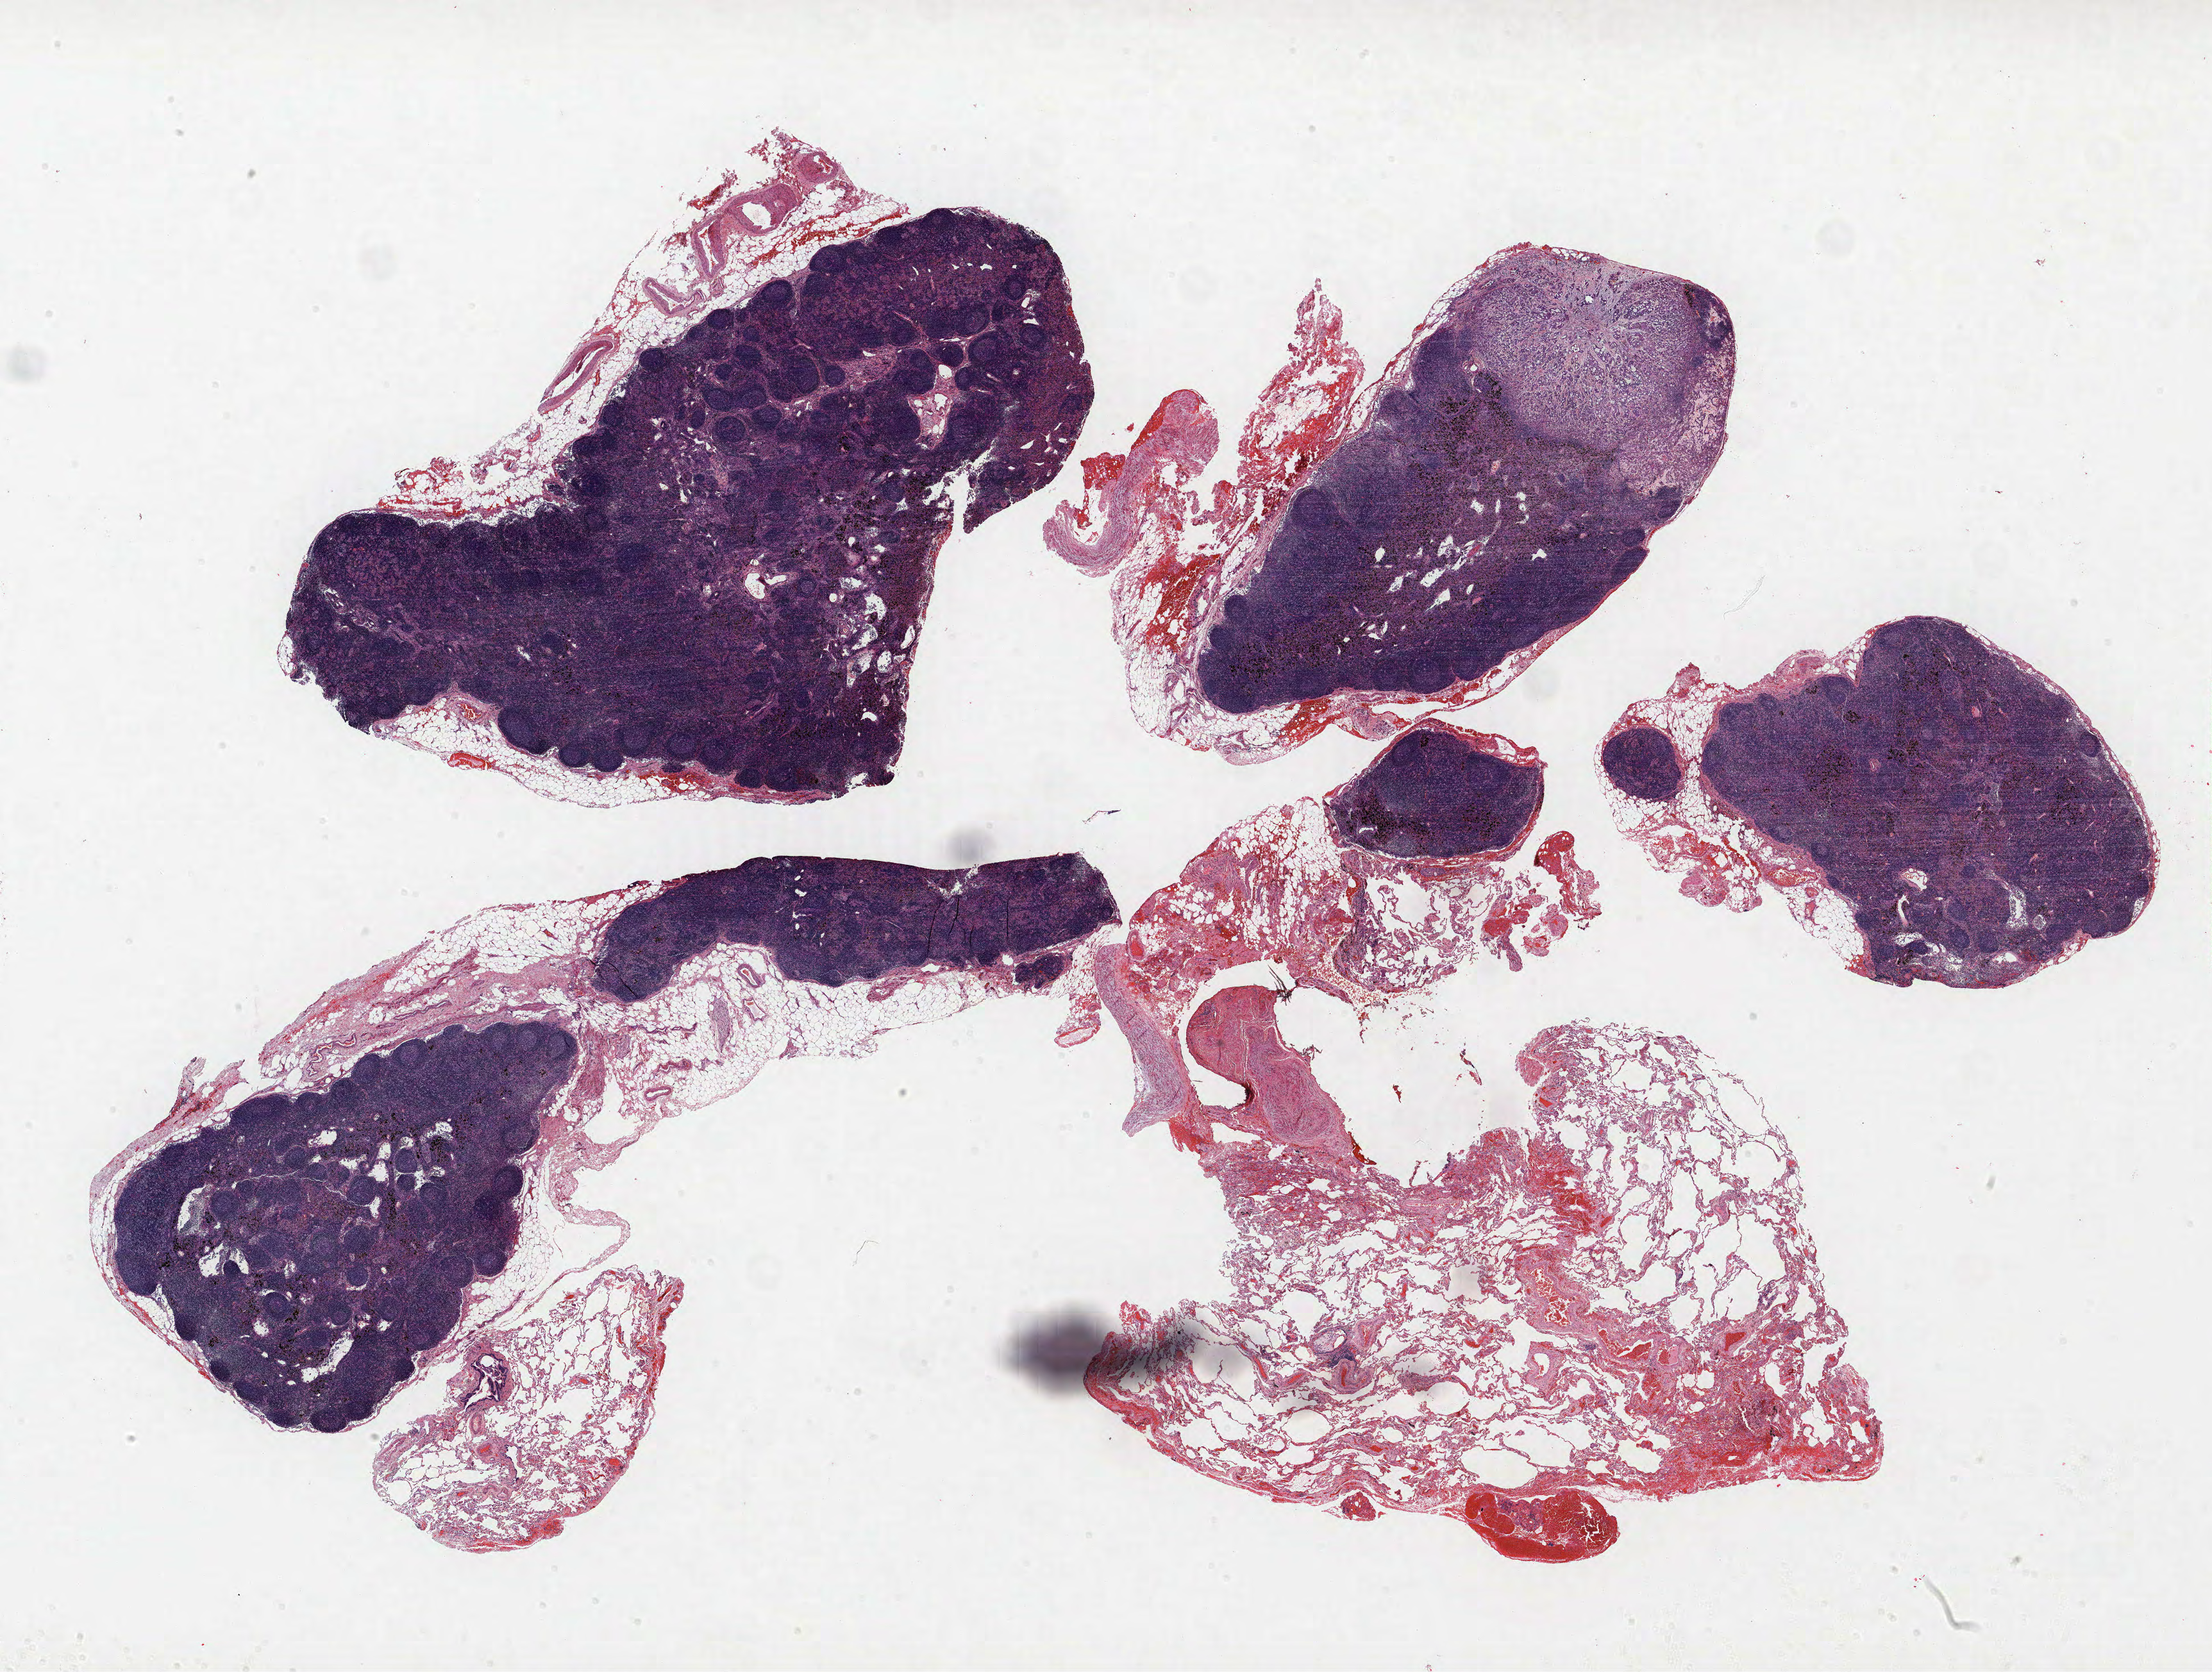
Whole-slide histology image, H&E, low-resolution overview of the scanned area, about 27.6 x 20.9 mm (acquisition: 40x scan), formalin-fixed paraffin-embedded (FFPE) section, lung. Female patient, aged 58 at enrolment. Former smoker at enrolment. Grade: moderately differentiated (G2).
* ICD-O-3 topography: upper lobe of lung (C34.1)
* stage (AJCC 6th edition): IIA
* tumour size (pathology): 15 mm
* participant's lung-cancer diagnosis: Adenocarcinoma, NOS
* primary tumour location (clinical record): left upper lobe